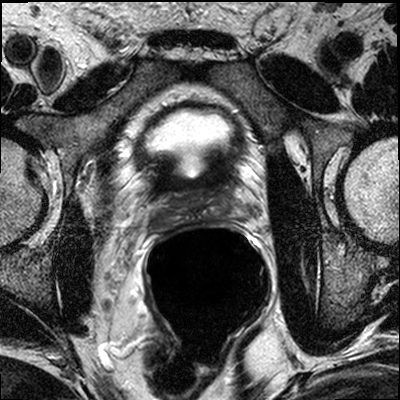
MRI of the prostate; 3 images, each a single mid-volume slice chosen by position (not for content). Treatment context recorded for this patient: No surgery, ADT with XRT.
Image 1: axial T2-weighted image, slice 17 of 32.
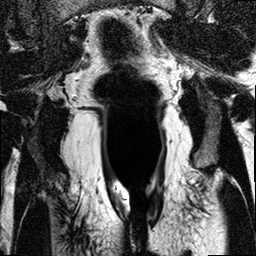
Image 2: T2-weighted coronal slice, slice 6 of 10, 3 mm slice thickness.
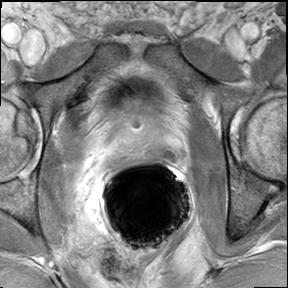
Image 3: axial dynamic contrast-enhanced (DCE) T1-weighted image, slice 17 of 32, dynamic phase 5 of 8, 6 mm slice thickness.
Radiologist's MRI report for this examination:
FINDINGS: The zonal anatomy is preserved. There is an aprrox. 2.3 x 1.7 cm mass seen in the right posterior and lateral peripheral zone of the mid third and apex with extension to the base. The mass abuts the obturator muscle and the right neurovascular bundle. Extracapsular extension at the right apex and beginning neurovascular involvement, as well as beginning involvement of the right obturator muscle are possible. There is a second smaller mass, 0.7 x 1.1 cm, seen in the left lateral peripheral zone, at the midthird and upper apical third of the prostate No evidence of extraprostatic extension on the left. No evidence for involvement of the left neurovascular bundle. No evidence for seminal vesicles infiltration. No evidence of involvement of bladder neck and rectal wall. No suspiciously enlarged obturator and iliac lymph nodes. Multiplanar reconstructions, subtraction images, and CAD analysis of the dynamic series for assessment of the kinetic information facilitated the interpretation of the exam. IMPRESSION: Bilateral cancer, with larger mass on the right, as detailed above. Extracapsular extension into apex and right neurovascular bundle is possible. Tumor also abuts the right obturator muscle. No evidence of infiltration of left neurovascular bundle or seminal vesicles. No local pelvic lymphadenopathy.

Prostate biopsy pathology (as recorded):
The specimen consists of multiple brown/tan core biopsies measuring in length from 1 cm up to 2 cm and 0.01 cm in diameter each. The specimen is submitted in toto in six cassettes as follows: 1 right PZ, 2 right PZ/TZ, 3 right apex, 4 left PZ, 5 left PZ/TZ, 6 left apex. PROSTATE 1. RIGHT PZ: PROSTATIC ADENOCARCINOMA, GLEASON SCORE 3+4=7/10, INVOLVING 2 CORES, 90% OF TISSUE EXAMINED. 2. RIGHT PZ/TZ: PROSTATIC ADENOCARCINOMA, GLEASON SCORE 4+3=7/10, INVOLVING 2 CORES, 90% OF TISSUE EXAMINED. 3. RIGHT APEX: PROSTATIC ADENOCARCINOMA, GLEASON SCORE 3+4=7/10, INVOLVING 2 CORES, 80% OF TISSUE EXAMINED. 4. LEFT PZ: PROSTATIC ADENOCARCINOMA, GLEASON SCORE 4+3=7/10, INVOLVING 2 CORES, 60% OF TISSUE EXAMINED. 5. LEFT PZ/TZ: PROSTATIC ADENOCARCINOMA, GLEASON SCORE 3+4=7/10, INVOLVING 2 CORES, 50% OF TISSUE EXAMINED. 6. LEFT APEX: PROSTATIC ADENOCARCINOMA, GLEASON SCORE 3+4=7/10, INVOLVING 2 CORES, 60% OF TISSUE EXAMINED.